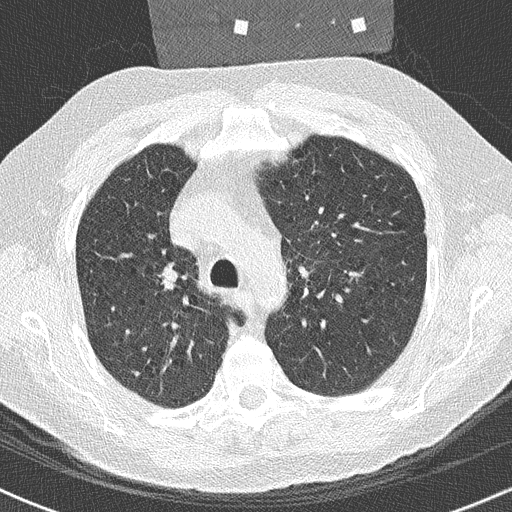
Chest CT (low-dose screening protocol), one axial image. First (baseline) screen. Lung window (W 1500 / L -600 HU). Slice 82 of 250 in the series. Male participant, aged 59 years at enrolment.
- Expert reader's lesion annotation, bounding box <147,258,182,295> (left, top, right, bottom; pixels).
- Screening reader's record for this exam: no non-calcified nodule ≥4 mm recorded.
- Official screen result: negative screen, minor abnormalities not suspicious for lung cancer.
- Later outcome: lung cancer diagnosed 360 days after this screen (after the second annual screen) — squamous cell carcinoma, NOS, right upper lobe, poorly differentiated (G3), stage IIA (AJCC 6th edition), 20 mm at pathology.